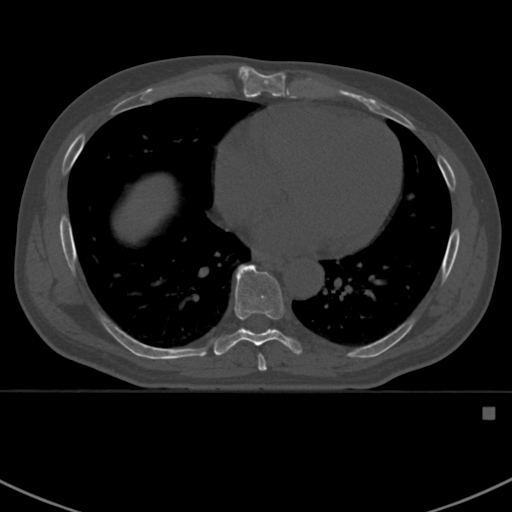
CT including the spine, one axial slice. Slice 400 of 412 in the series (ordered by position). Reconstruction kernel Br40s. 120 kVp. Bone window (W 1800 / L 400 HU). 512 × 512 image matrix, field of view 358 × 358 mm. Patient: male, 59 years. Case-level facts recorded for this patient, not image findings: primary cancer: prostate.
Outlined on this slice (semi-automatic segmentation, software-assisted and operator-edited):
- T7 vertebra: bounding box [x1, y1, x2, y2] px = [258, 355, 267, 371]
- T8 vertebra: [214, 264, 301, 356]